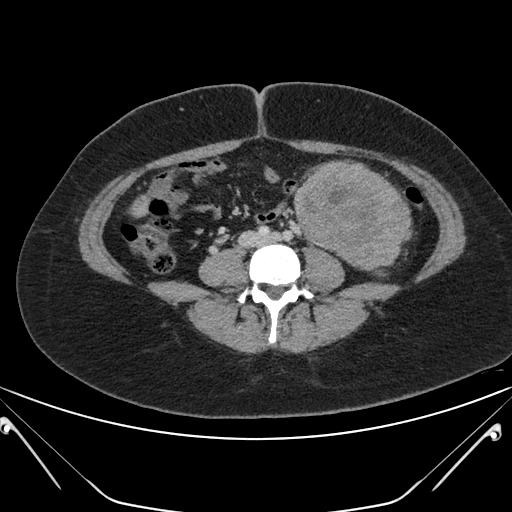
Contrast-enhanced abdominal CT, one axial slice. Position 78 of 168 along the scan axis. 120 kVp. Soft-tissue window (W 400 / L 40 HU). 3 mm slice thickness. 512 × 512 image matrix, field of view 394 × 394 mm. Patient: female, 26 years. From the clinical record (not read from this slice): diagnosis: adrenocortical carcinoma; tumour side: left adrenal; tumour size at pathology: 28 cm.
Outlined on this slice (semi-automatic segmentation, software-assisted and operator-edited):
- mass: bounding box [x1, y1, x2, y2] px = [294, 161, 411, 267]